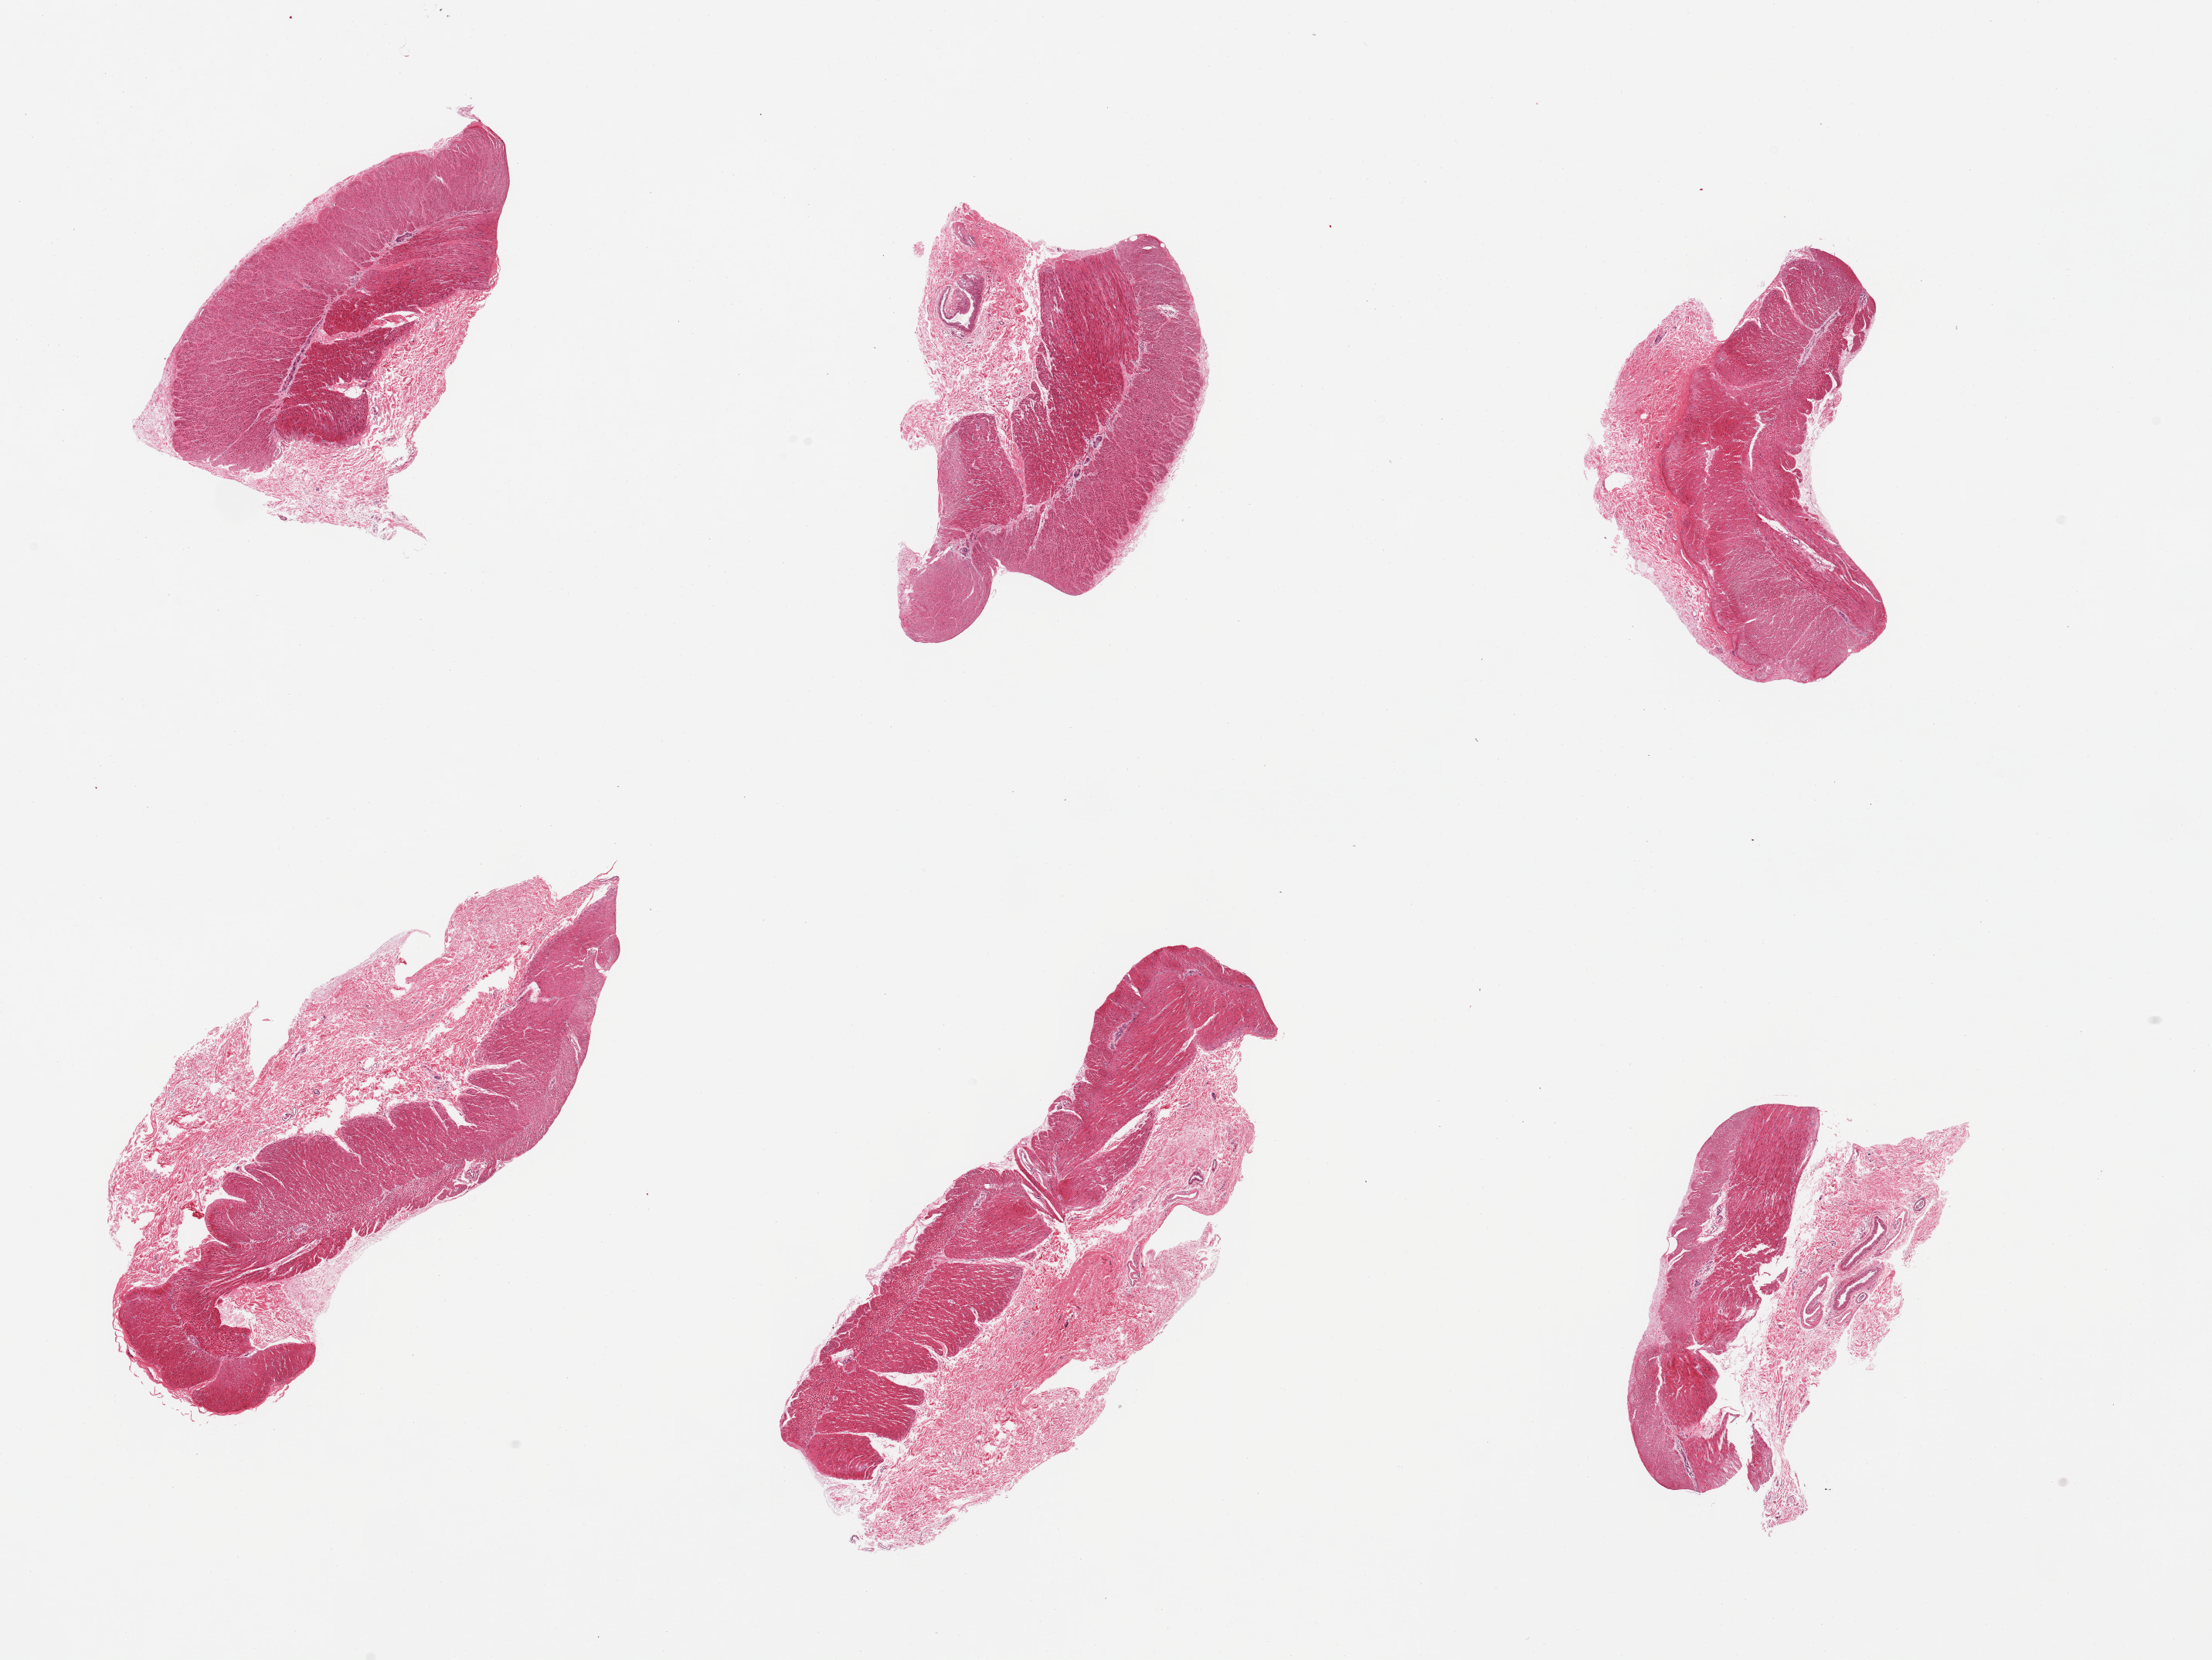
Whole-slide image, H&E stain — whole scanned area (about 22.6 x 17.0 mm, from a 20x scan) shown as a low-resolution overview. PAXgene-fixed, paraffin-embedded tissue. Target tissue: transverse colon. Tissue donor sample. Male donor.
Pathologist's review note for this sample: 6 pieces, mucosa sloughed.